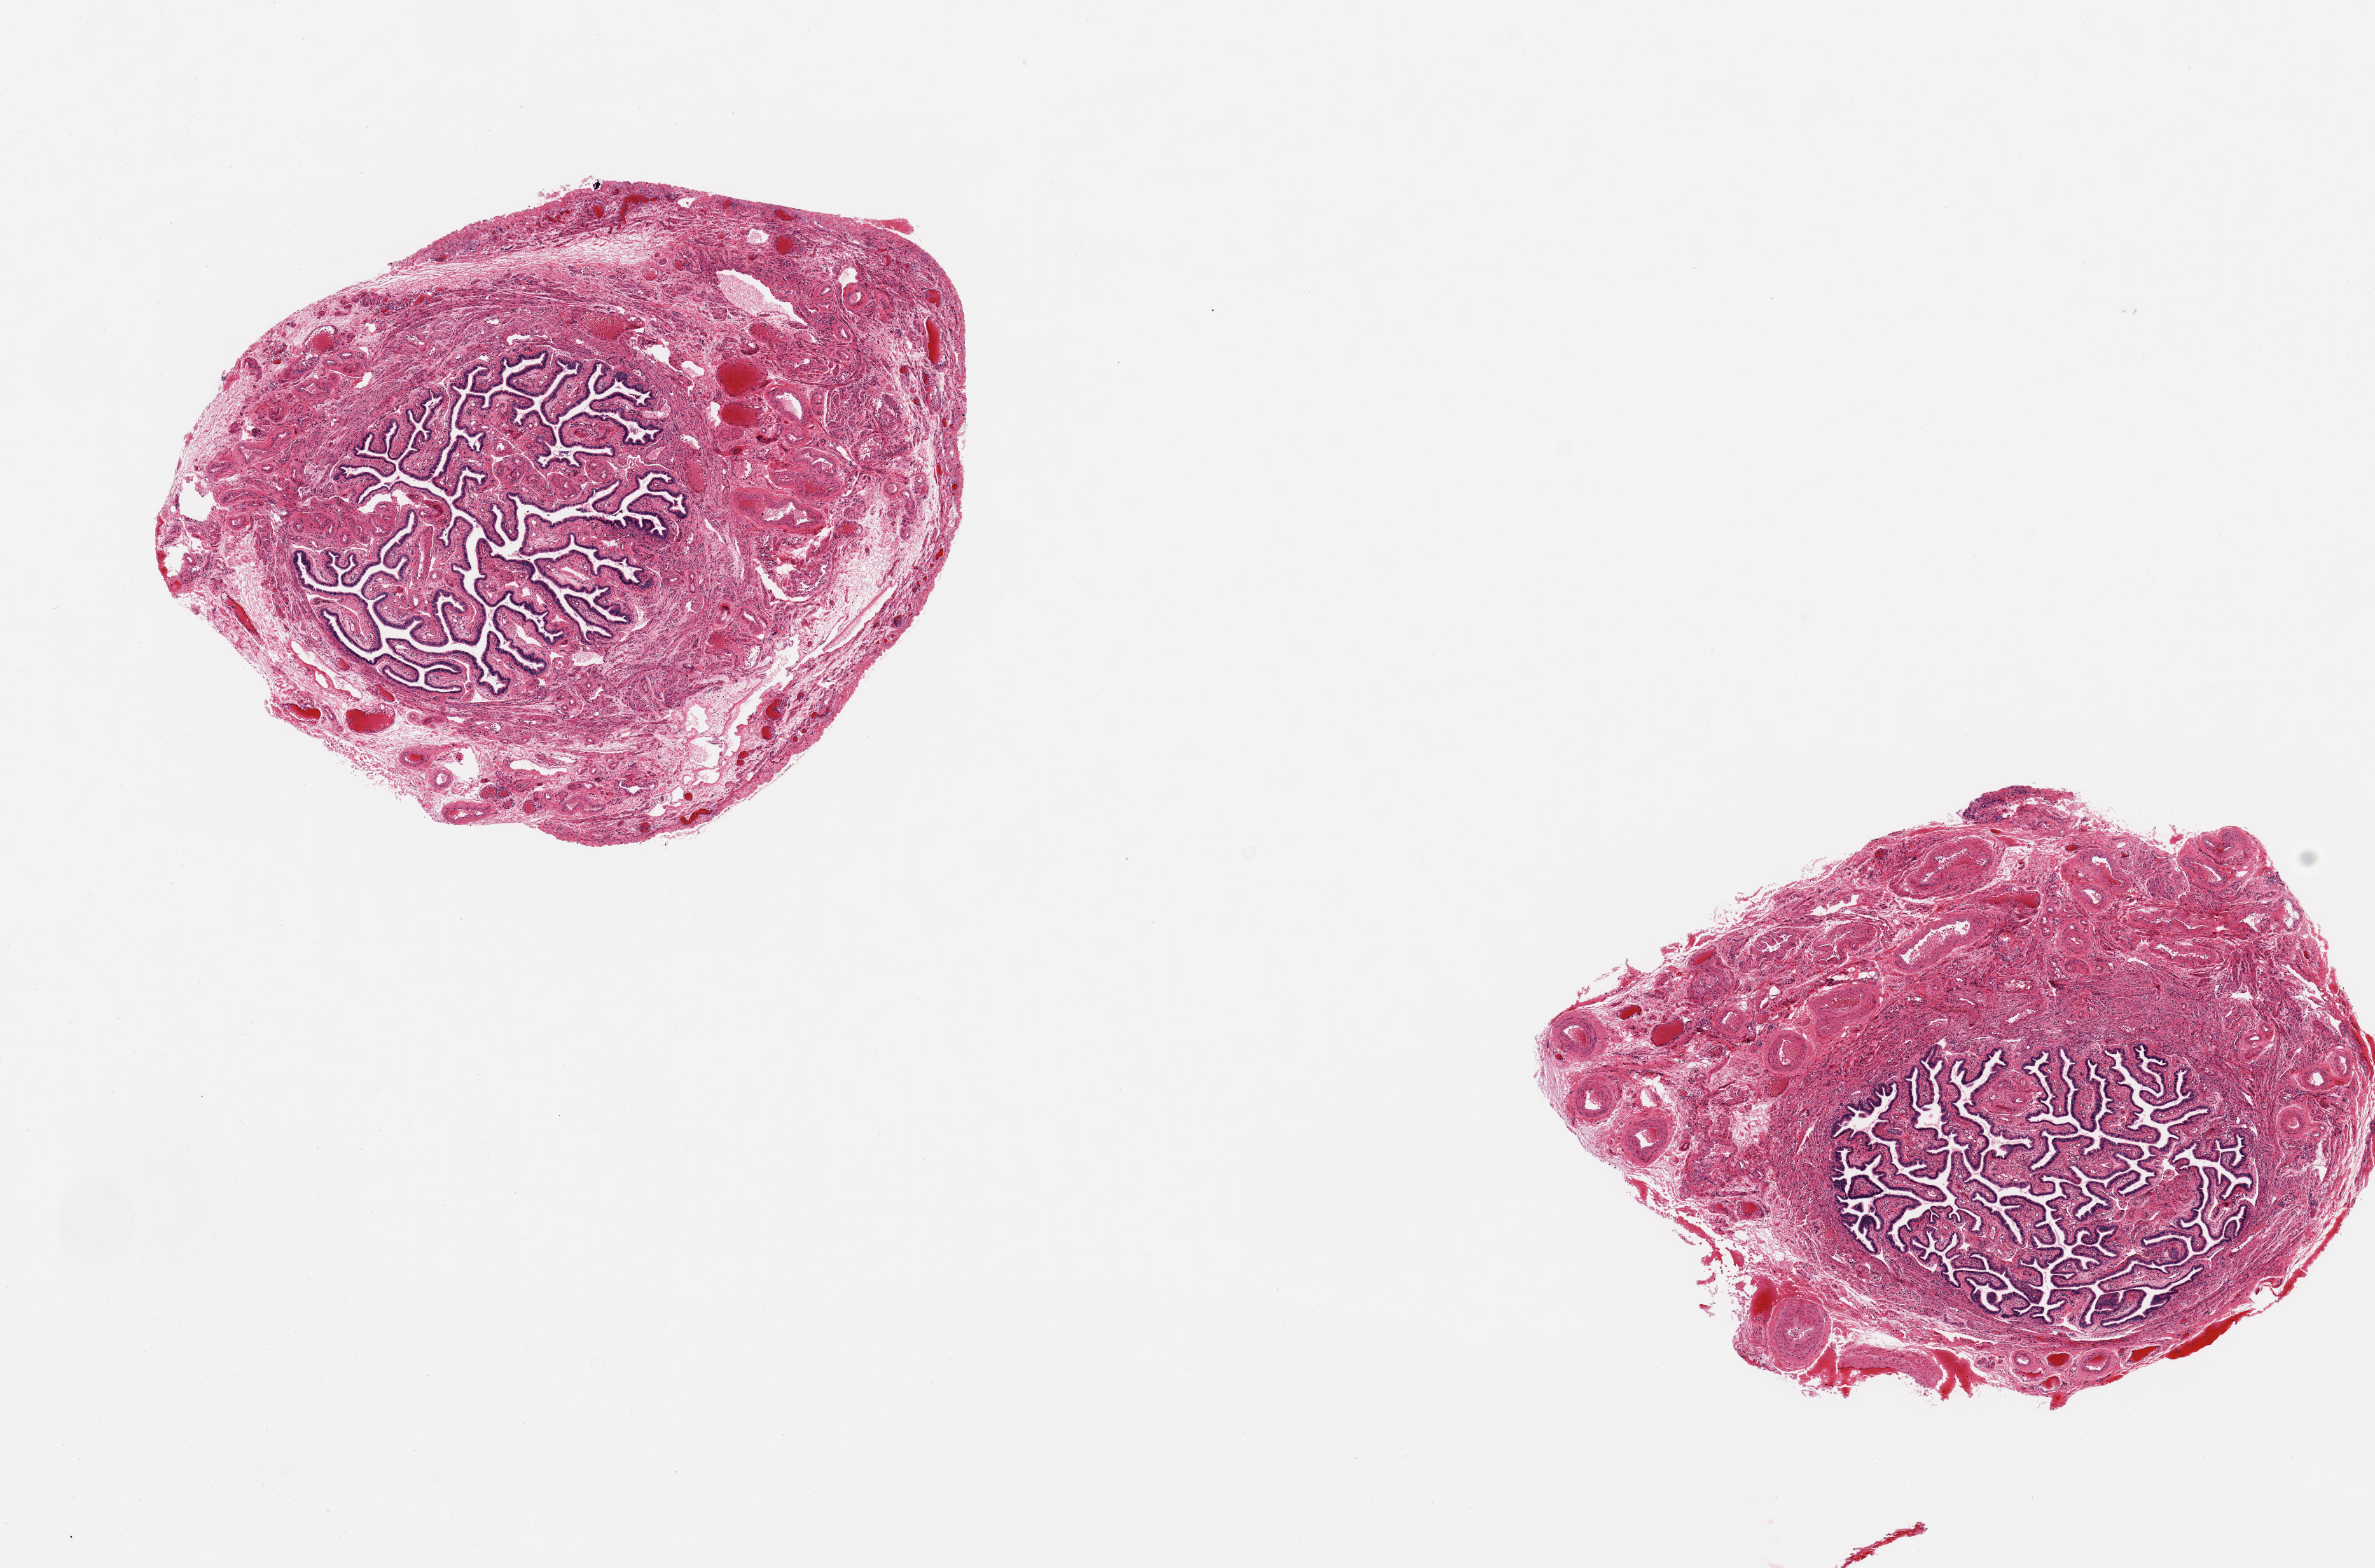
Whole-slide image, haematoxylin and eosin stain — low-resolution overview of the scanned area, about 14.8 x 9.8 mm (slide scanned at 20x). PAXgene-fixed, paraffin-embedded tissue. Sampled site (target tissue): fallopian tube. Tissue donor sample.
Review note (as recorded): 2 aliquots, ~ 4.5mm d. Mucosa extremely well preserved.